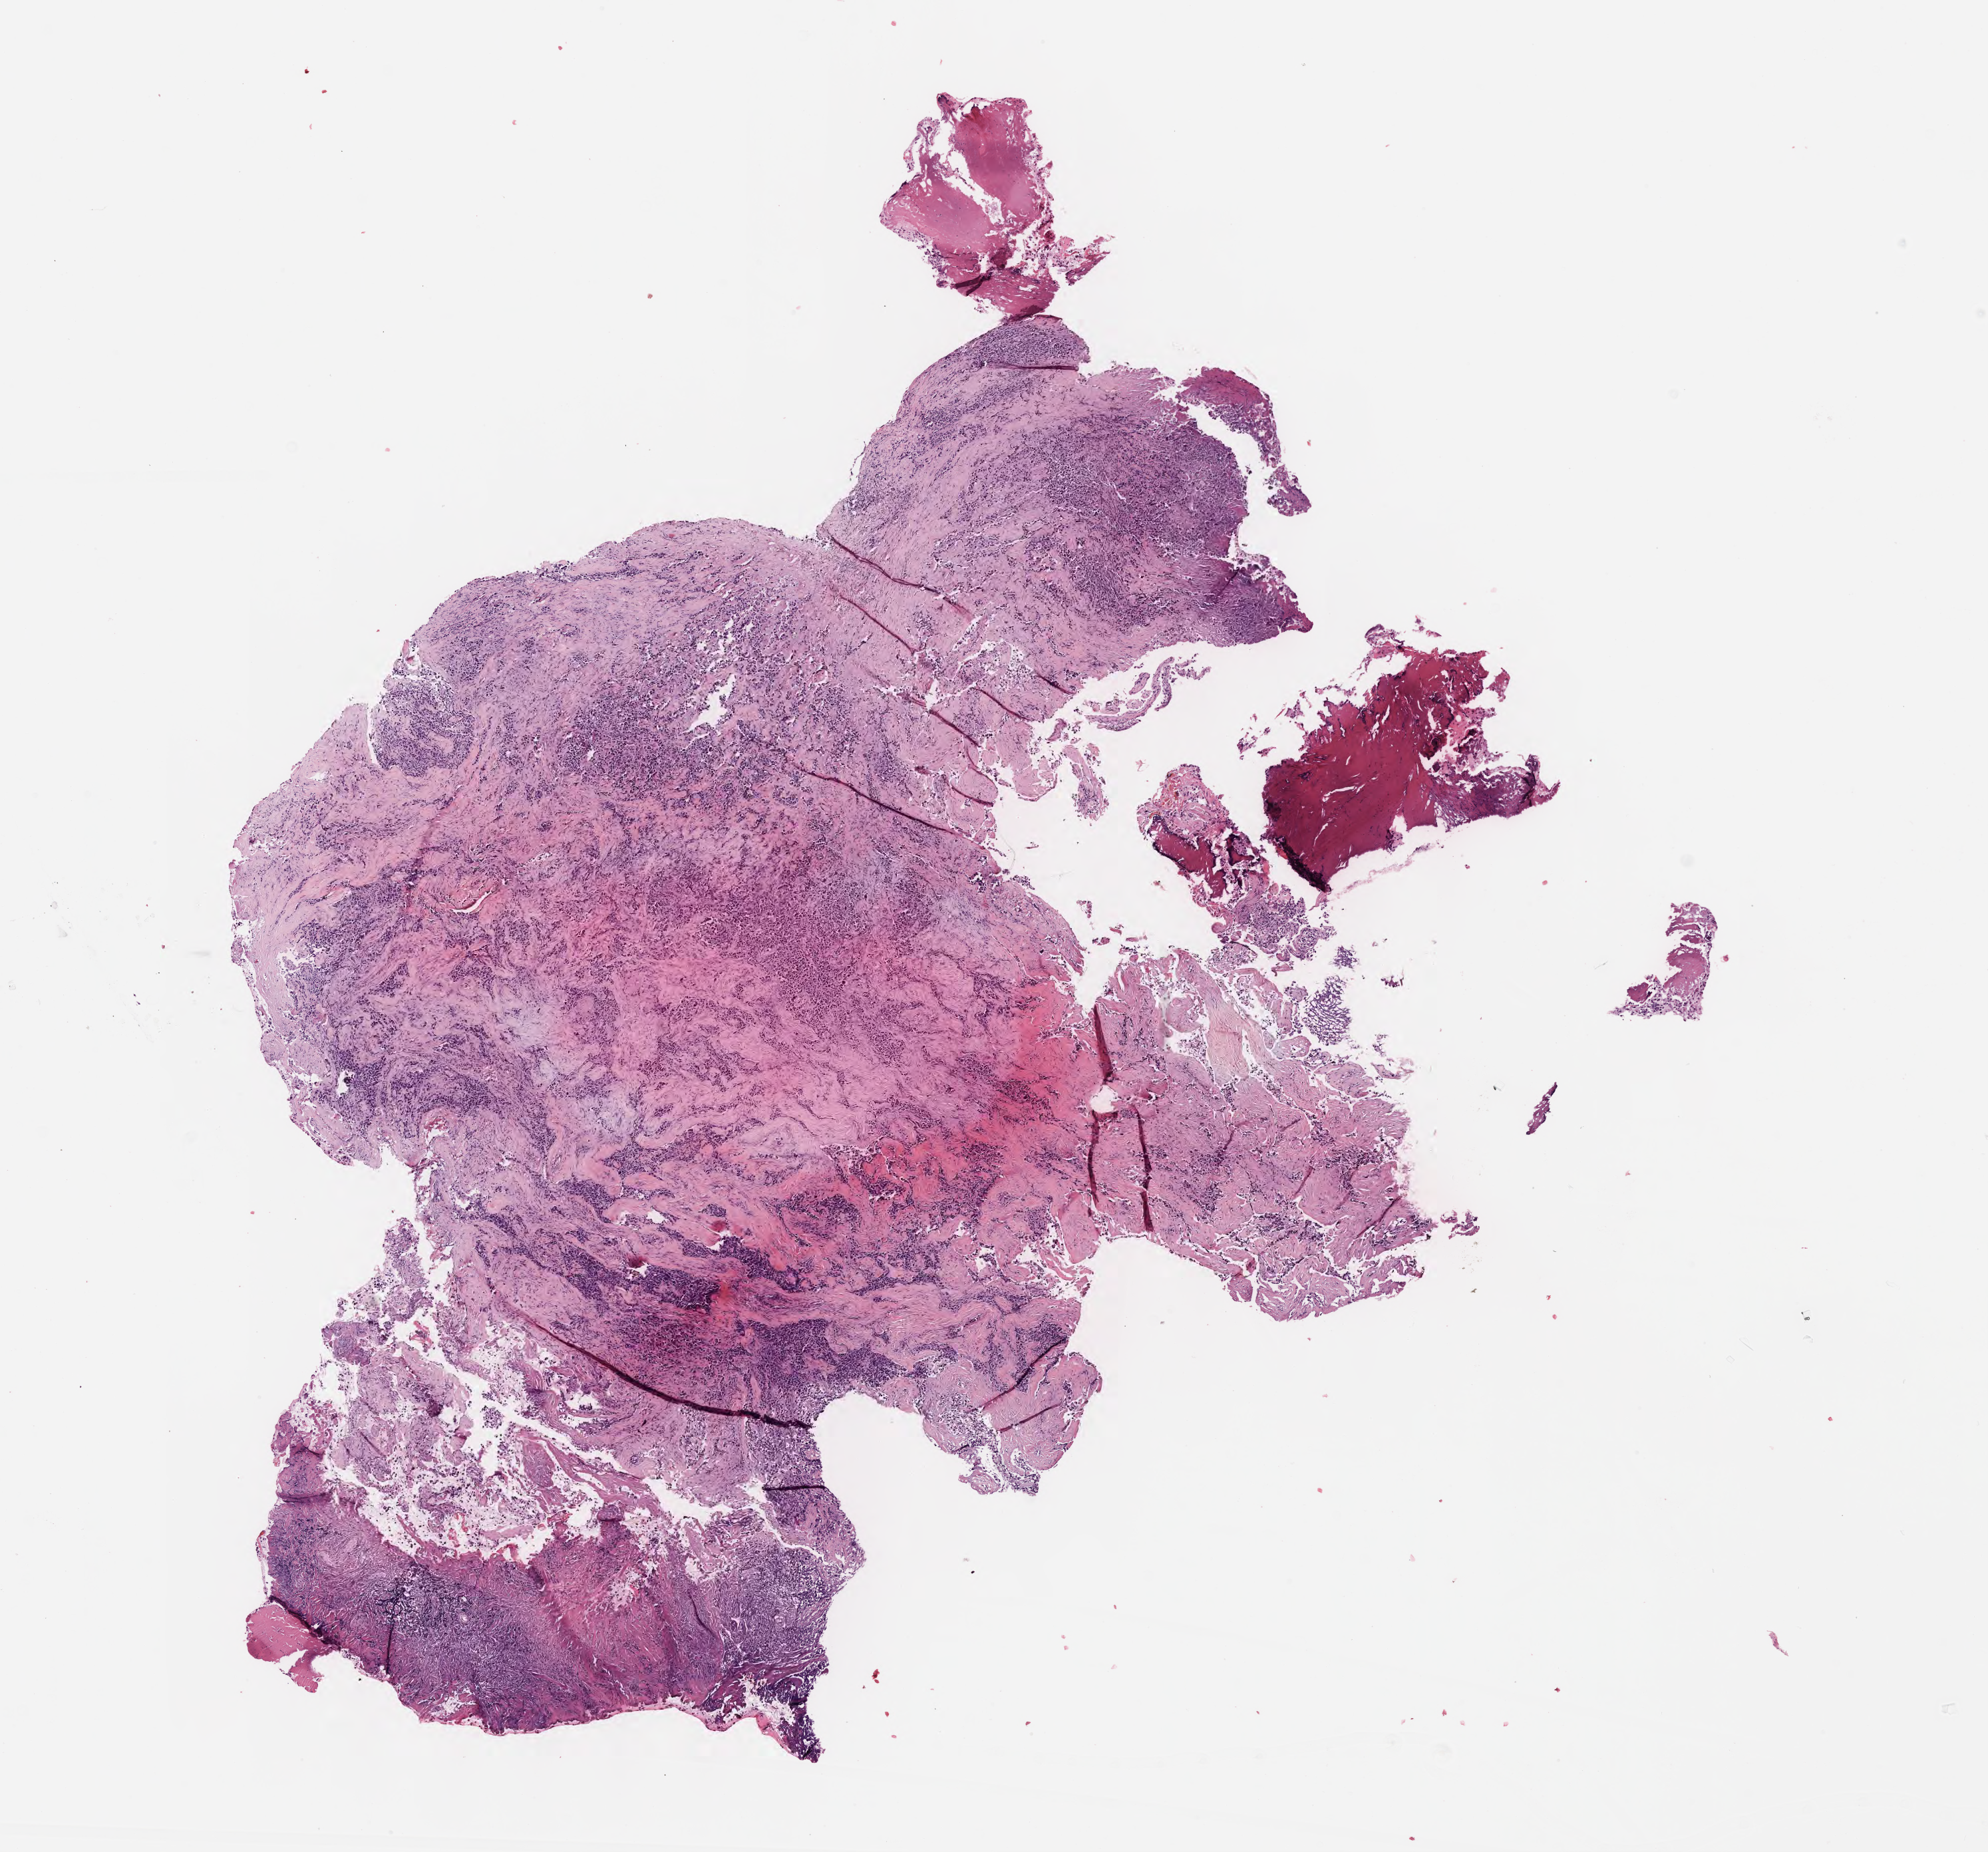
Digitized Hematoxylin and eosin (H&E) stained tissue section (whole slide) — shown as a low-resolution overview of the whole scanned area (about 12.1 x 11.2 mm), formalin-fixed paraffin-embedded (FFPE) diagnostic section, mesothelium, primary tumour sample. Male patient; age at initial diagnosis 60 years.
AJCC pathologic stage: III. Diagnosis: Epithelioid mesothelioma, malignant.